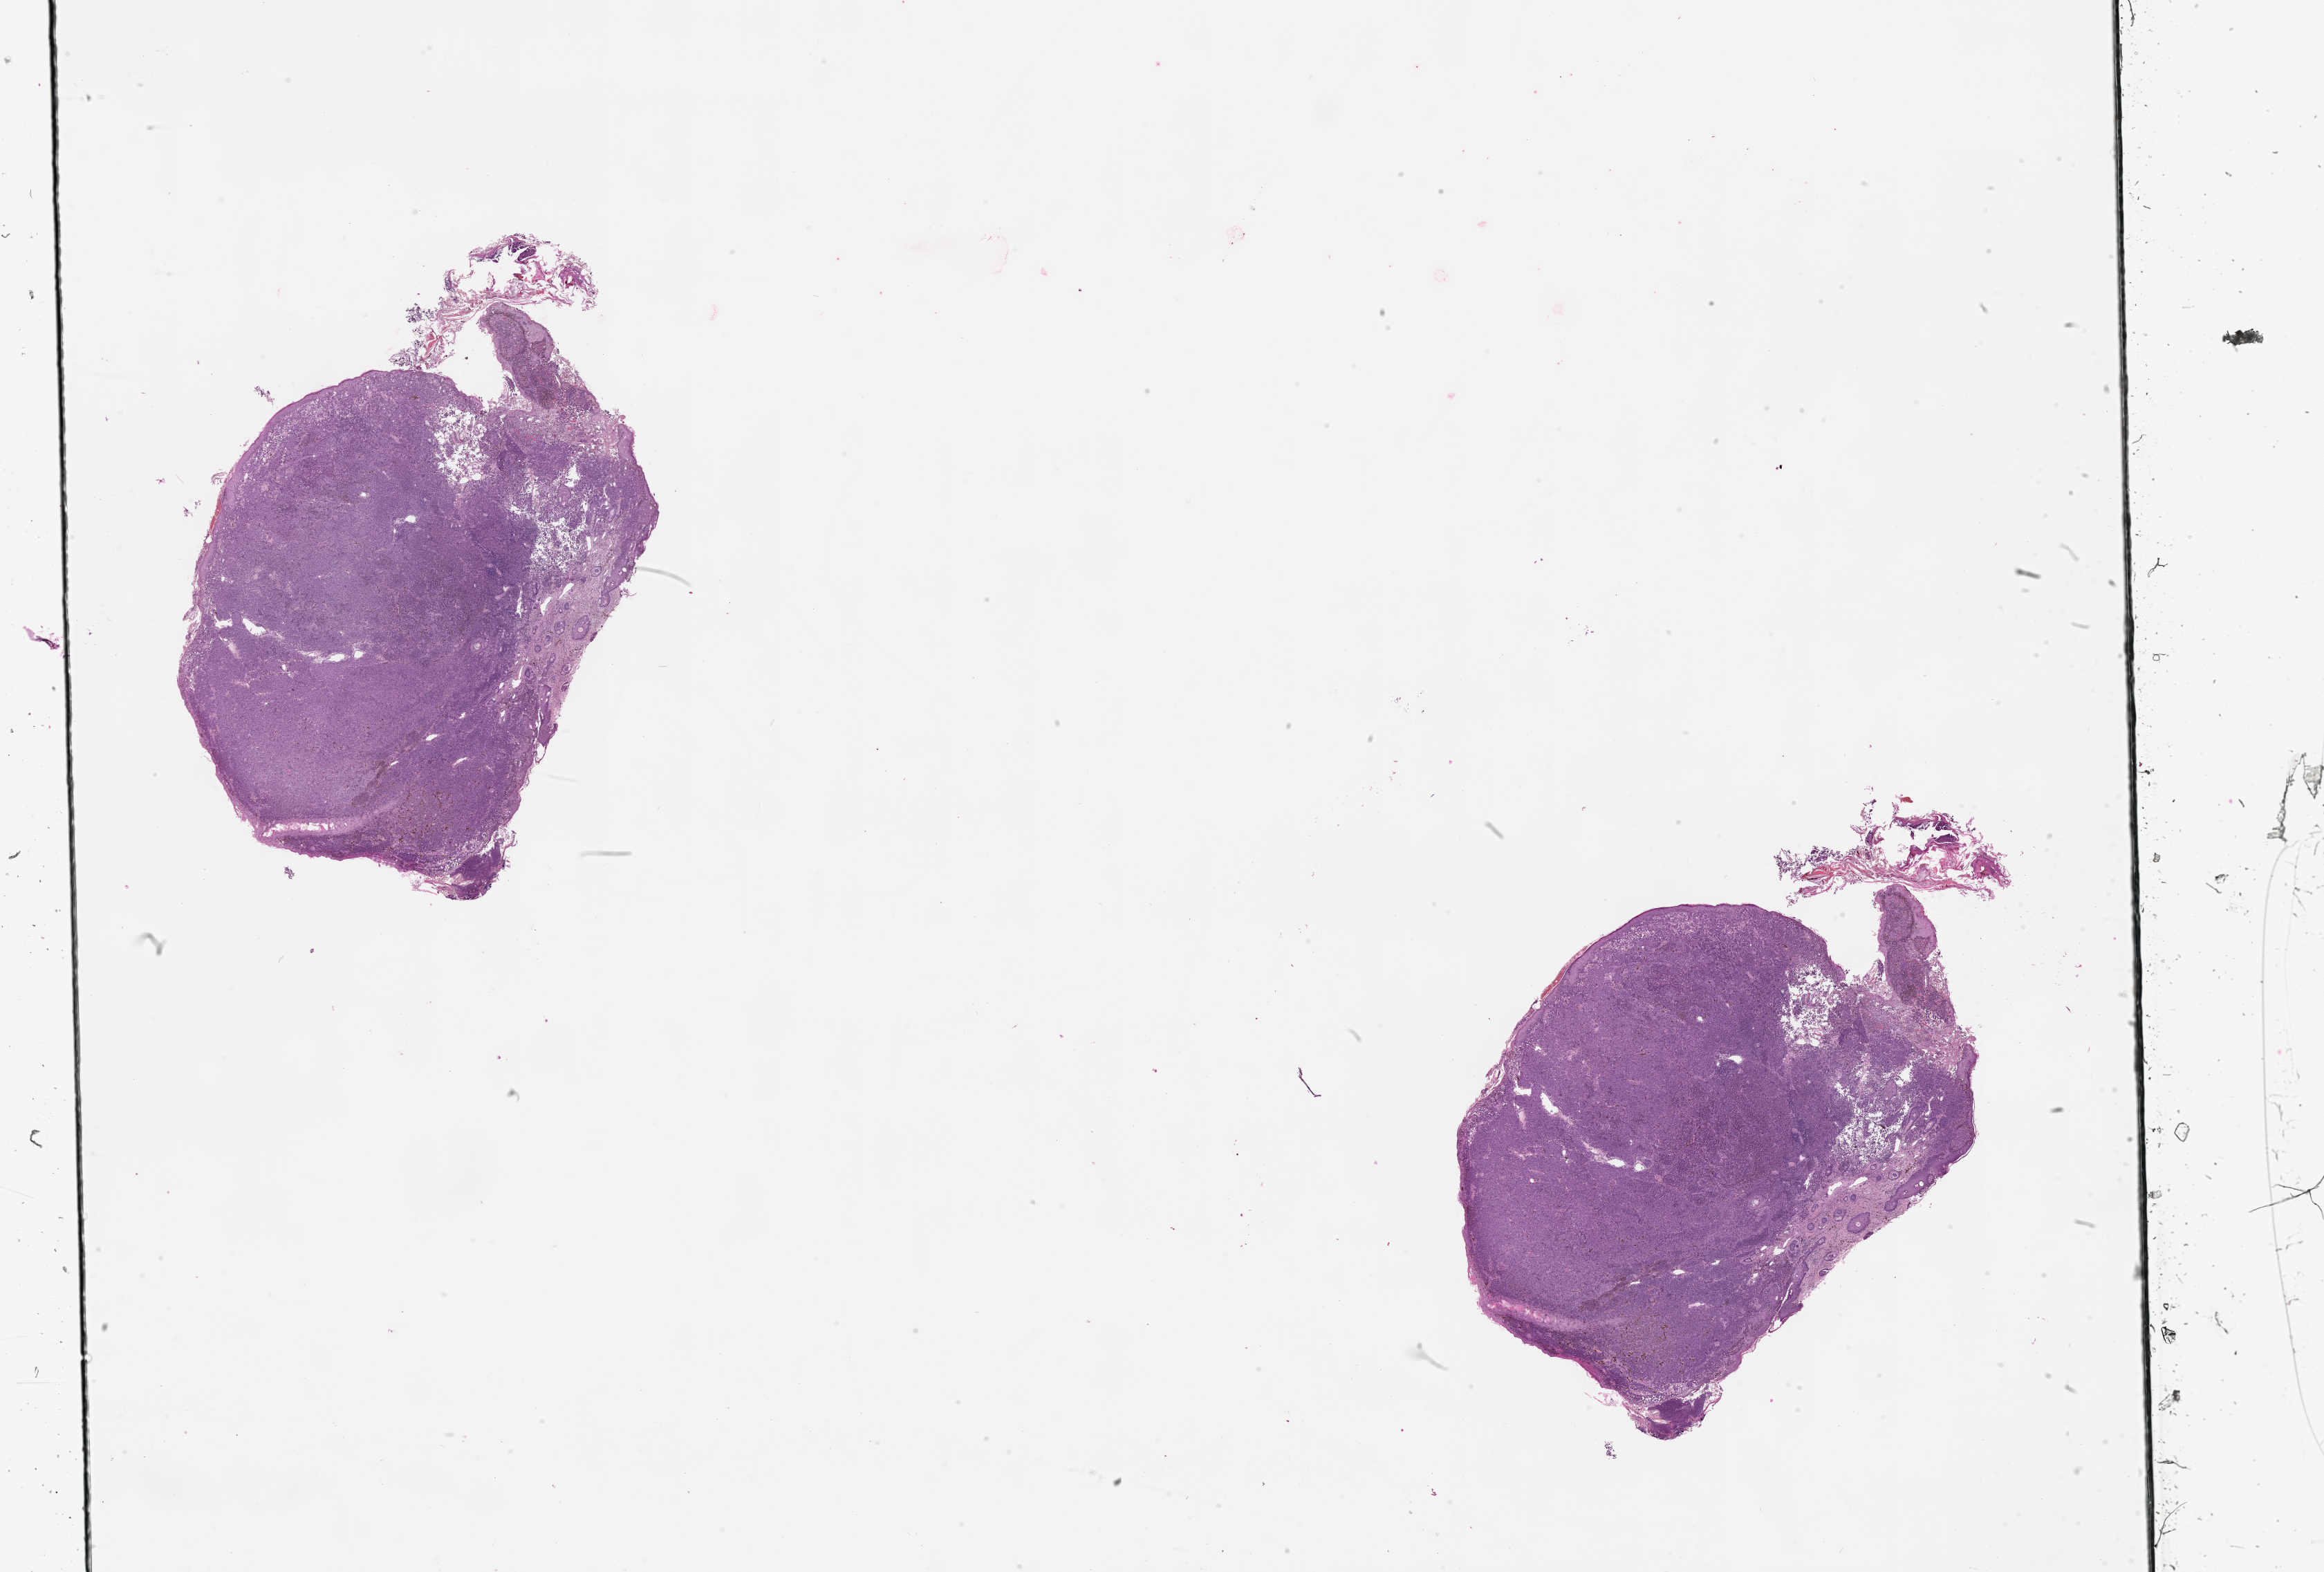
Whole-slide histology image, H&E — a low-resolution overview of the entire scanned area, about 27.1 x 18.3 mm. Tumour tissue sample, sampled site: head & neck. Patient: female, age 75 years. Composition of this section per pathologist review: tumour nuclei 80%, necrosis 0%.
AJCC pathologic stage: IIC. Histologic diagnosis: Malignant melanoma, NOS.